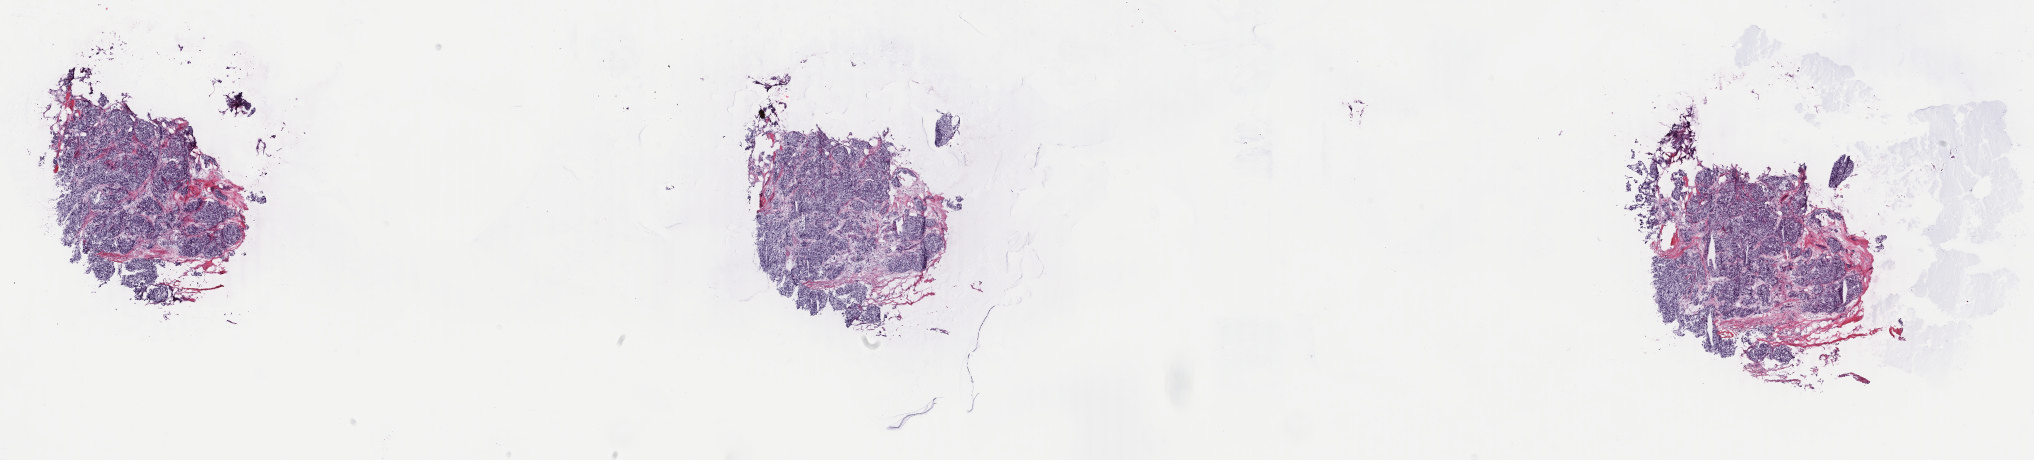
Whole-slide histology image, H&E-stained, a low-resolution overview of the entire scanned area, about 32.4 x 7.3 mm (slide scanned at 40x). Frozen section from the top of the tissue portion. Sample: primary tumour, breast. Female, age 45 years at initial diagnosis. Slide review estimates, as recorded: tumour cells 90%, tumour nuclei 90%, normal cells 0%, stromal cells 10%, necrosis 0%. Inflammatory infiltration, as recorded: lymphocyte infiltration 1%, monocyte infiltration 0%, neutrophil infiltration 0%.
* pathologic diagnosis: Infiltrating duct mixed with other types of carcinoma